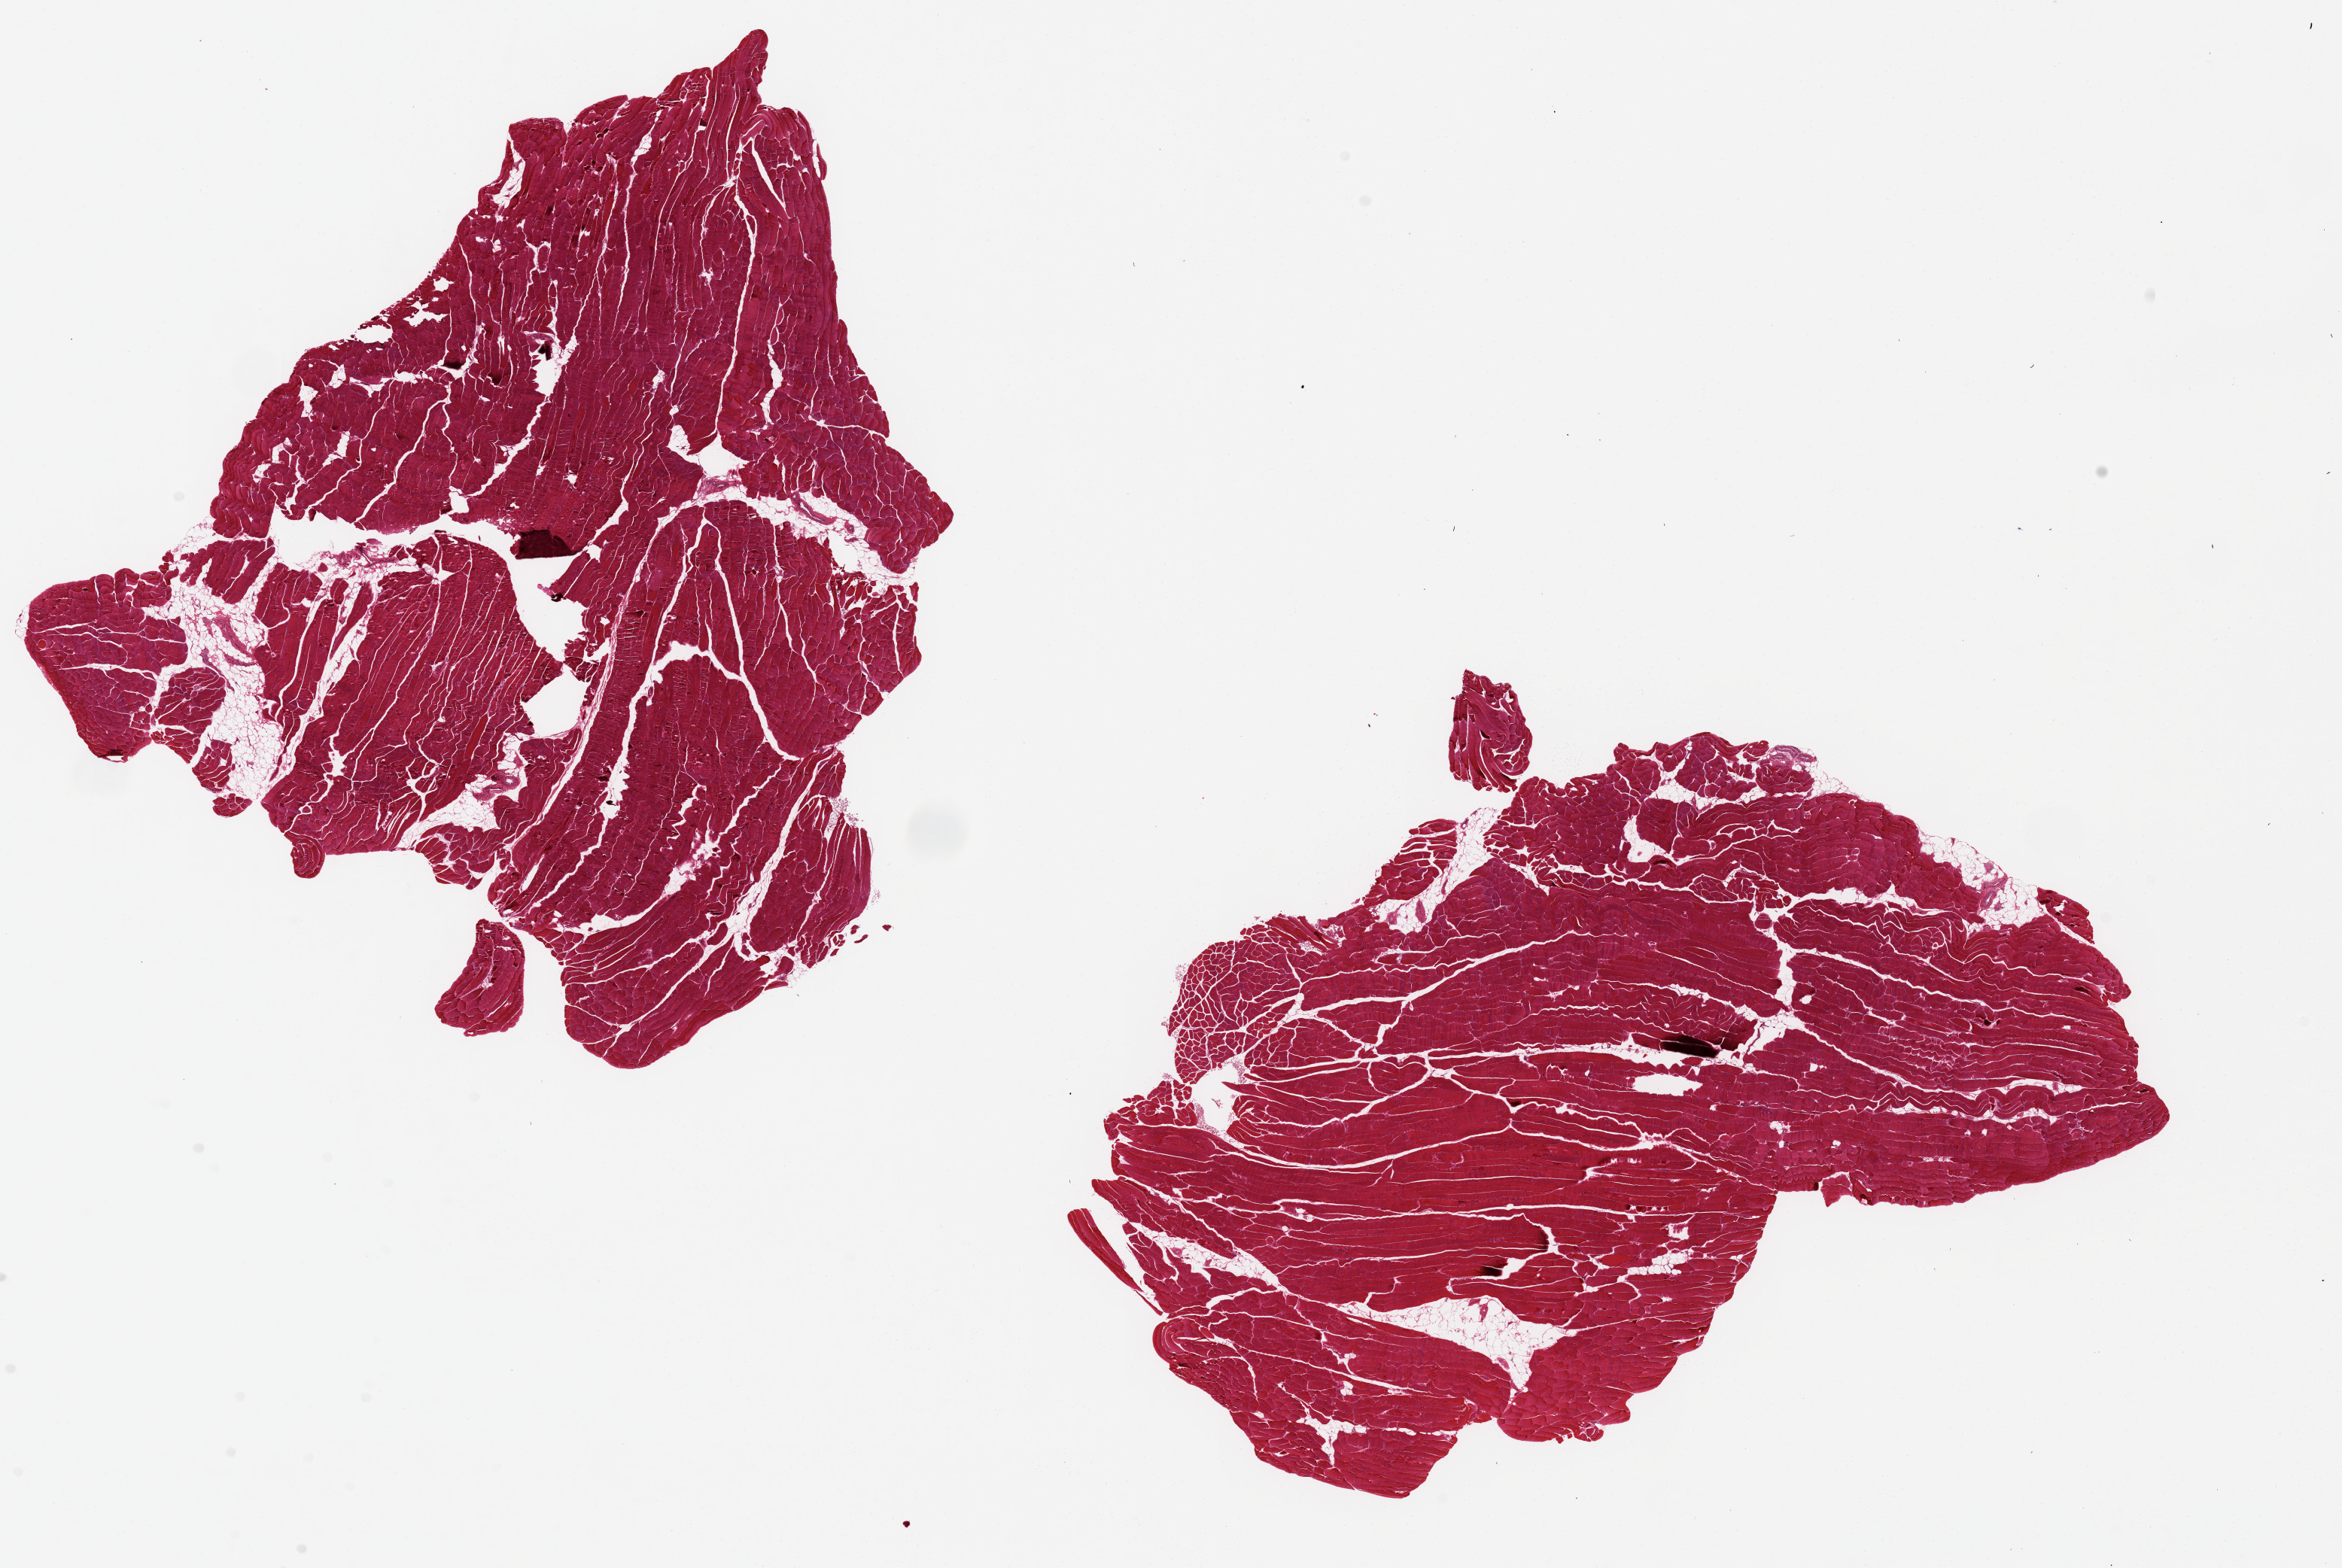
Digitized haematoxylin and eosin-stained section — shown as a low-resolution overview of the whole scanned area (about 24.6 x 16.5 mm), PAXgene-fixed paraffin-embedded (PFPE) section, sampled site (target tissue): skeletal muscle, tissue donor sample. Female donor.
- review note (as recorded): 2 pieces ~10x8mm. Minimal interstitial fat